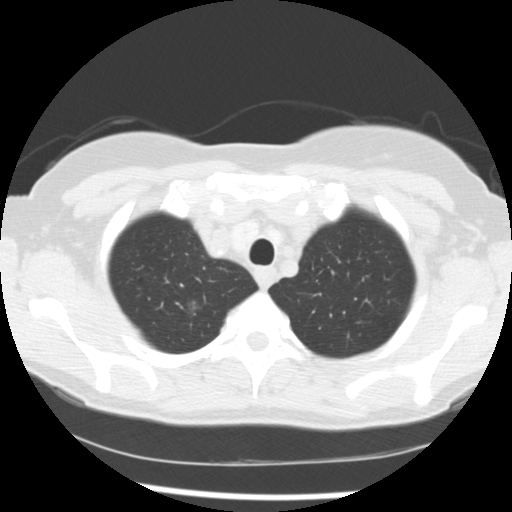
Low-dose screening chest CT, axial slice. First (baseline) screen. Lung window (W 1500 / L -600 HU). 2.5 mm slice thickness. 120 kVp. 512 × 512 image matrix. Female participant, aged 60 years at enrolment. Former smoker at enrolment.
Expert reader's lesion annotation, bounding box <163,288,216,334> (left, top, right, bottom; pixels). The screening reader recorded 3 non-calcified nodules or masses ≥4 mm on this exam (right upper lobe, right middle lobe, left lower lobe); which of them this box marks is not recorded. Official screen result: positive, change unspecified: nodule(s) >= 4 mm or enlarging nodule(s), mass(es), or other non-specific abnormalities suspicious for lung cancer.